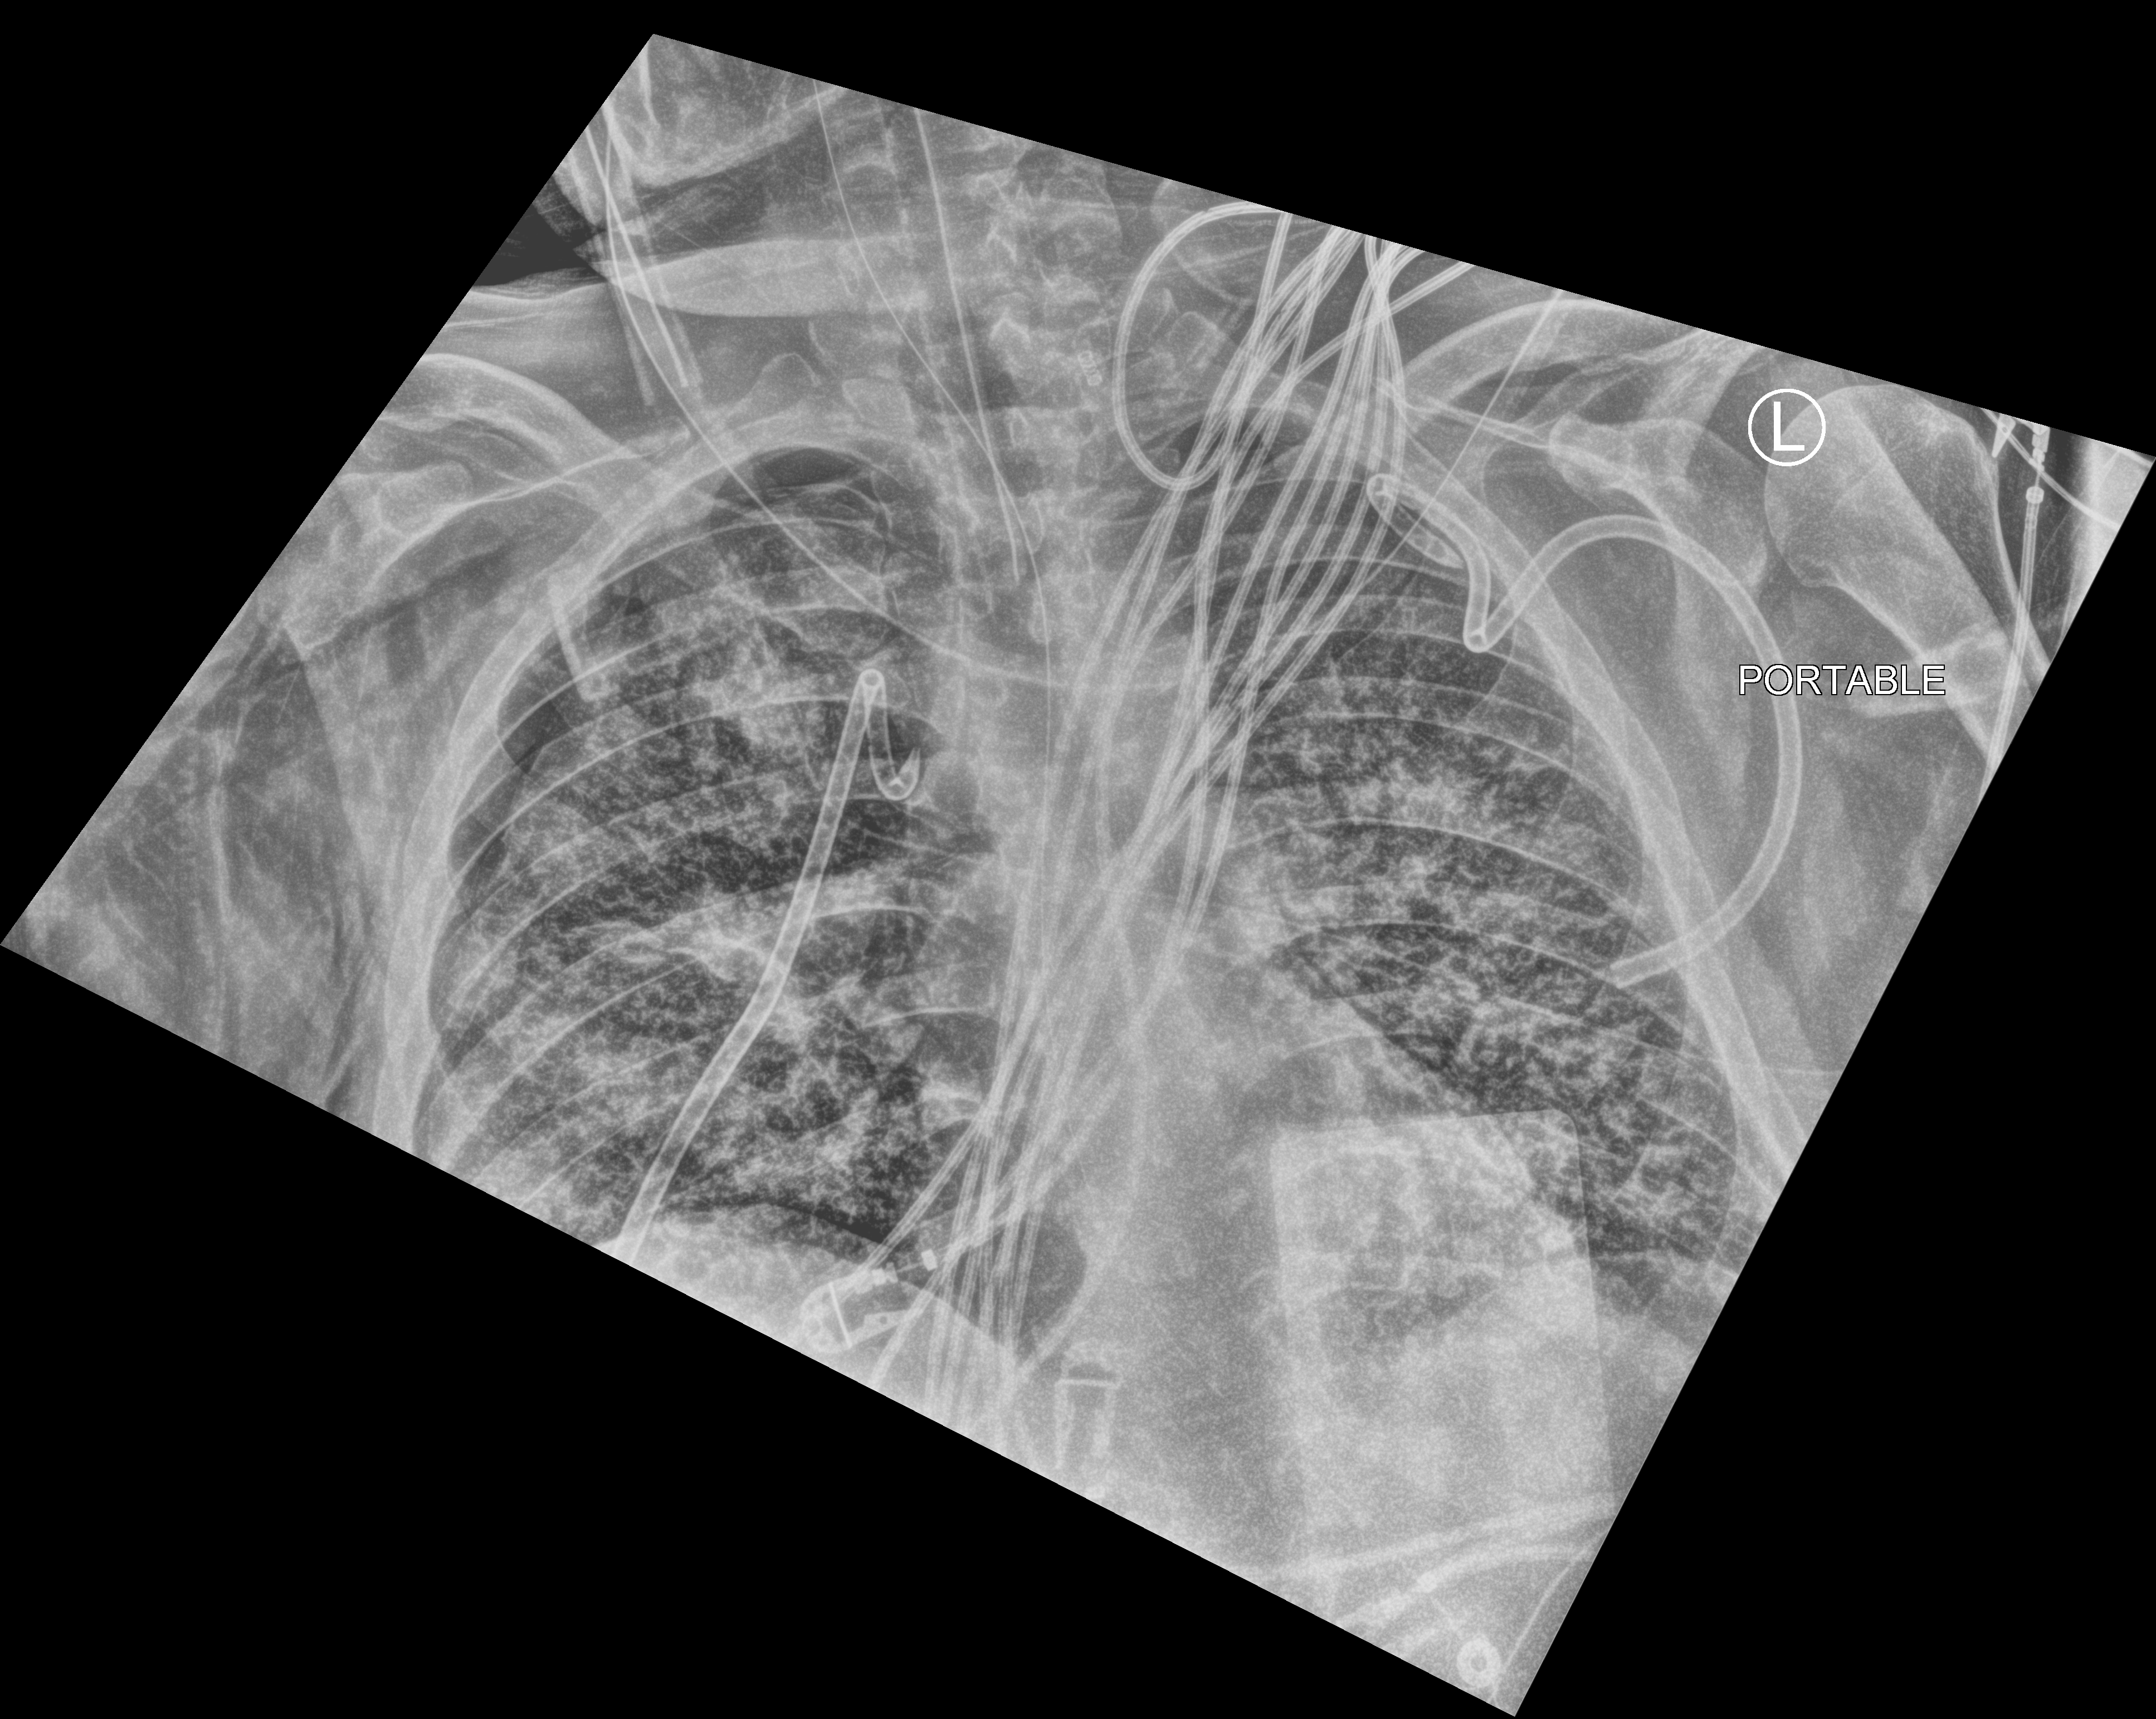
Bedside chest radiograph (computed radiography), anteroposterior (AP) projection. Adult patient hospitalised with COVID-19, age 18–59 years.
From the hospital-stay record, not from the radiograph (when in the stay this image was taken is not recorded): admitted to intensive care during this hospital stay: yes; mechanically ventilated during this hospital stay: yes.